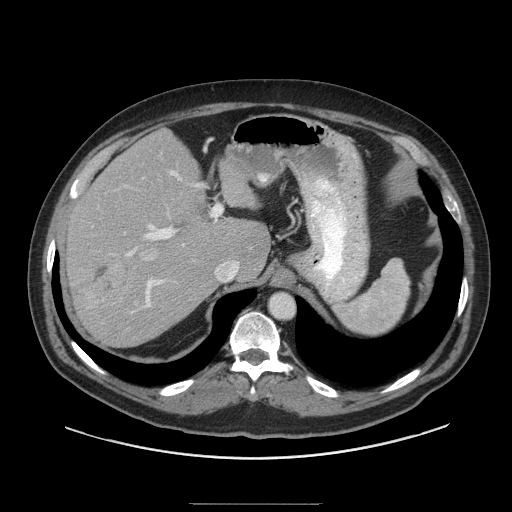
Contrast-enhanced abdominal CT (liver protocol), one axial slice. Soft-tissue window (W 400 / L 40 HU). 512 × 512 image matrix. Case-level facts recorded for this patient, not image findings: diagnosis: hepatocellular carcinoma (patient treated with transarterial chemoembolisation; whether this scan precedes or follows treatment is not stated here); TNM stage (as recorded): Stage-I; Child-Pugh class: A; tumour differentiation: well differentiated; tumour nodularity: uninodular.
Annotated regions visible in this slice (semi-automatically segmented with operator editing):
- abdominal aorta: box from (x=271, y=294) to (x=294, y=318) px
- liver parenchyma outside the tumour (the mass and vessels are separate outlines, so this box may not span the whole liver): (x=64, y=128)–(x=270, y=346)
- mass: (x=88, y=256)–(x=138, y=306)
- liver vessels: (x=126, y=171)–(x=217, y=308)